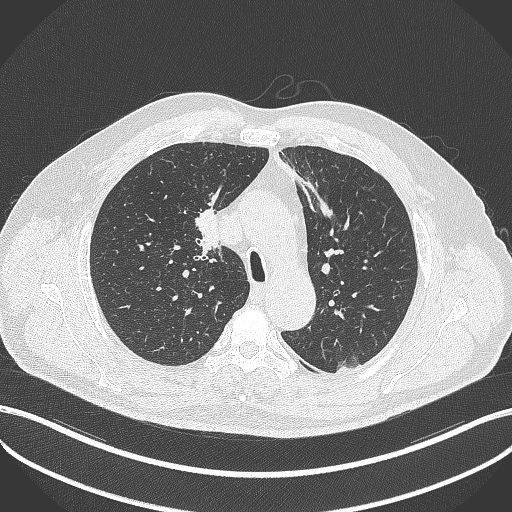
Chest CT, one axial slice; slice 275 of 411 in the series (ordered by position); reconstruction kernel B70f; 120 kVp; lung window (W 1500 / L -600 HU); 512 × 512 image matrix, field of view 400 × 400 mm. Male patient, age 60 years. Case-level facts recorded for this patient, not image findings: clinical TNM (as recorded): T1b N1 M0.
Structures marked on this image (bounding box drawn by a radiologist):
- lung tumour (recorded histology: squamous cell carcinoma): bounding box <191,206,225,253> (left, top, right, bottom; pixels)